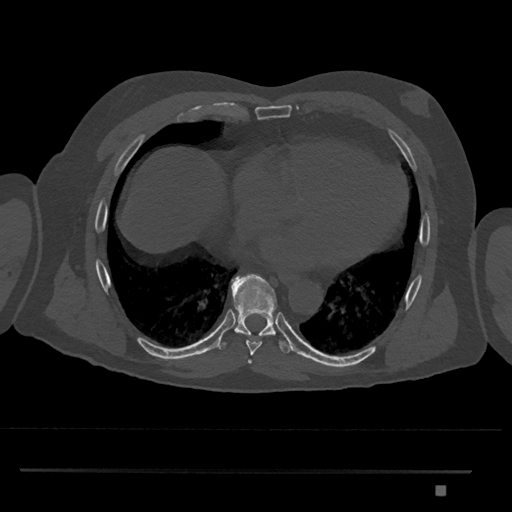
CT including the spine, one axial slice; 120 kVp; bone window (W 1800 / L 400 HU); 0.5 mm slice thickness; 512 × 512 image matrix, field of view 429 × 429 mm. Male patient, age 65 years. From the clinical record (not read from this slice): primary cancer: prostate.
Outlined on this slice (semi-automatic segmentation, software-assisted and operator-edited):
- T8 vertebra: bounding box (x1, y1, x2, y2) in pixels: (217, 274, 291, 355)